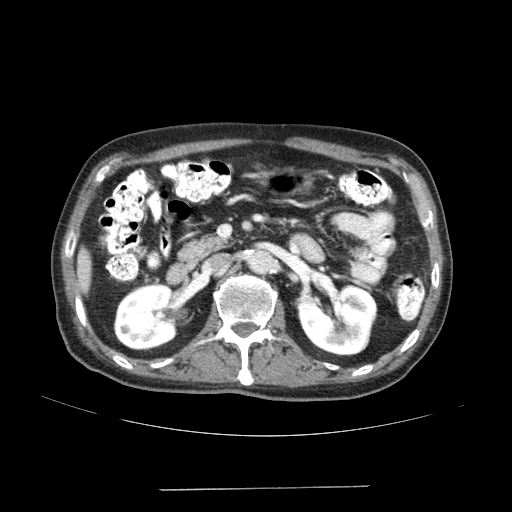
Contrast-enhanced abdominal CT (liver protocol), one axial slice. Slice 56 of 192 in the series (ordered by position). Reconstruction kernel SOFT. 120 kVp. Soft-tissue window (W 400 / L 40 HU). 512 × 512 image matrix, field of view 400 × 400 mm. From the clinical record (not read from this slice): diagnosis: hepatocellular carcinoma (patient treated with transarterial chemoembolisation; whether this scan precedes or follows treatment is not stated here); TNM stage (as recorded): Stage-IVA; Child-Pugh class: A; tumour differentiation: poorly differentiated; tumour nodularity: uninodular.
Outlined on this slice (semi-automatic segmentation, software-assisted and operator-edited):
- liver parenchyma outside the tumour (the mass and vessels are separate outlines, so this box may not span the whole liver): bounding box [x1, y1, x2, y2] px = [76, 248, 90, 292]